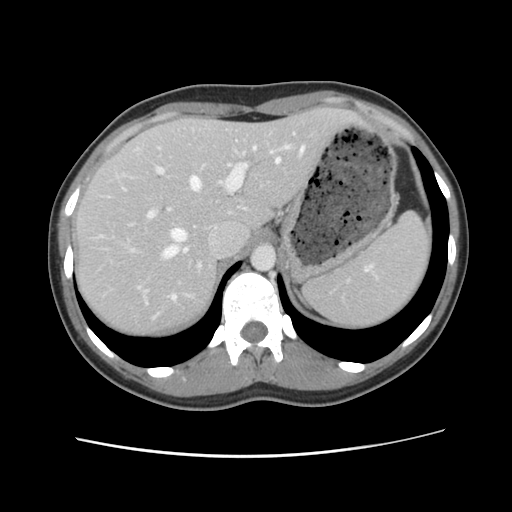
Contrast-enhanced abdominal CT, one axial slice; position 84 of 134 along the scan axis; 120 kVp; intravenous contrast given; soft-tissue window (W 400 / L 40 HU); 2.5 mm slice thickness; 512 × 512 image matrix, field of view 339 × 339 mm. Female patient, age 33 years. From the clinical record (not read from this slice): diagnosis: colorectal cancer liver metastases, imaged before liver resection; multiple liver metastases: yes; largest metastasis: 4.5 cm; disease in both lobes: yes.
Annotated regions visible in this slice (outlined manually by an expert reader):
- hepatic veins: bounding box <140,147,304,300> (left, top, right, bottom; pixels)
- liver: <73,109,356,338>
- planned liver remnant (the part of the liver to remain after resection): <75,109,356,338>
- portal vein (with intrahepatic branches): <148,139,294,218>